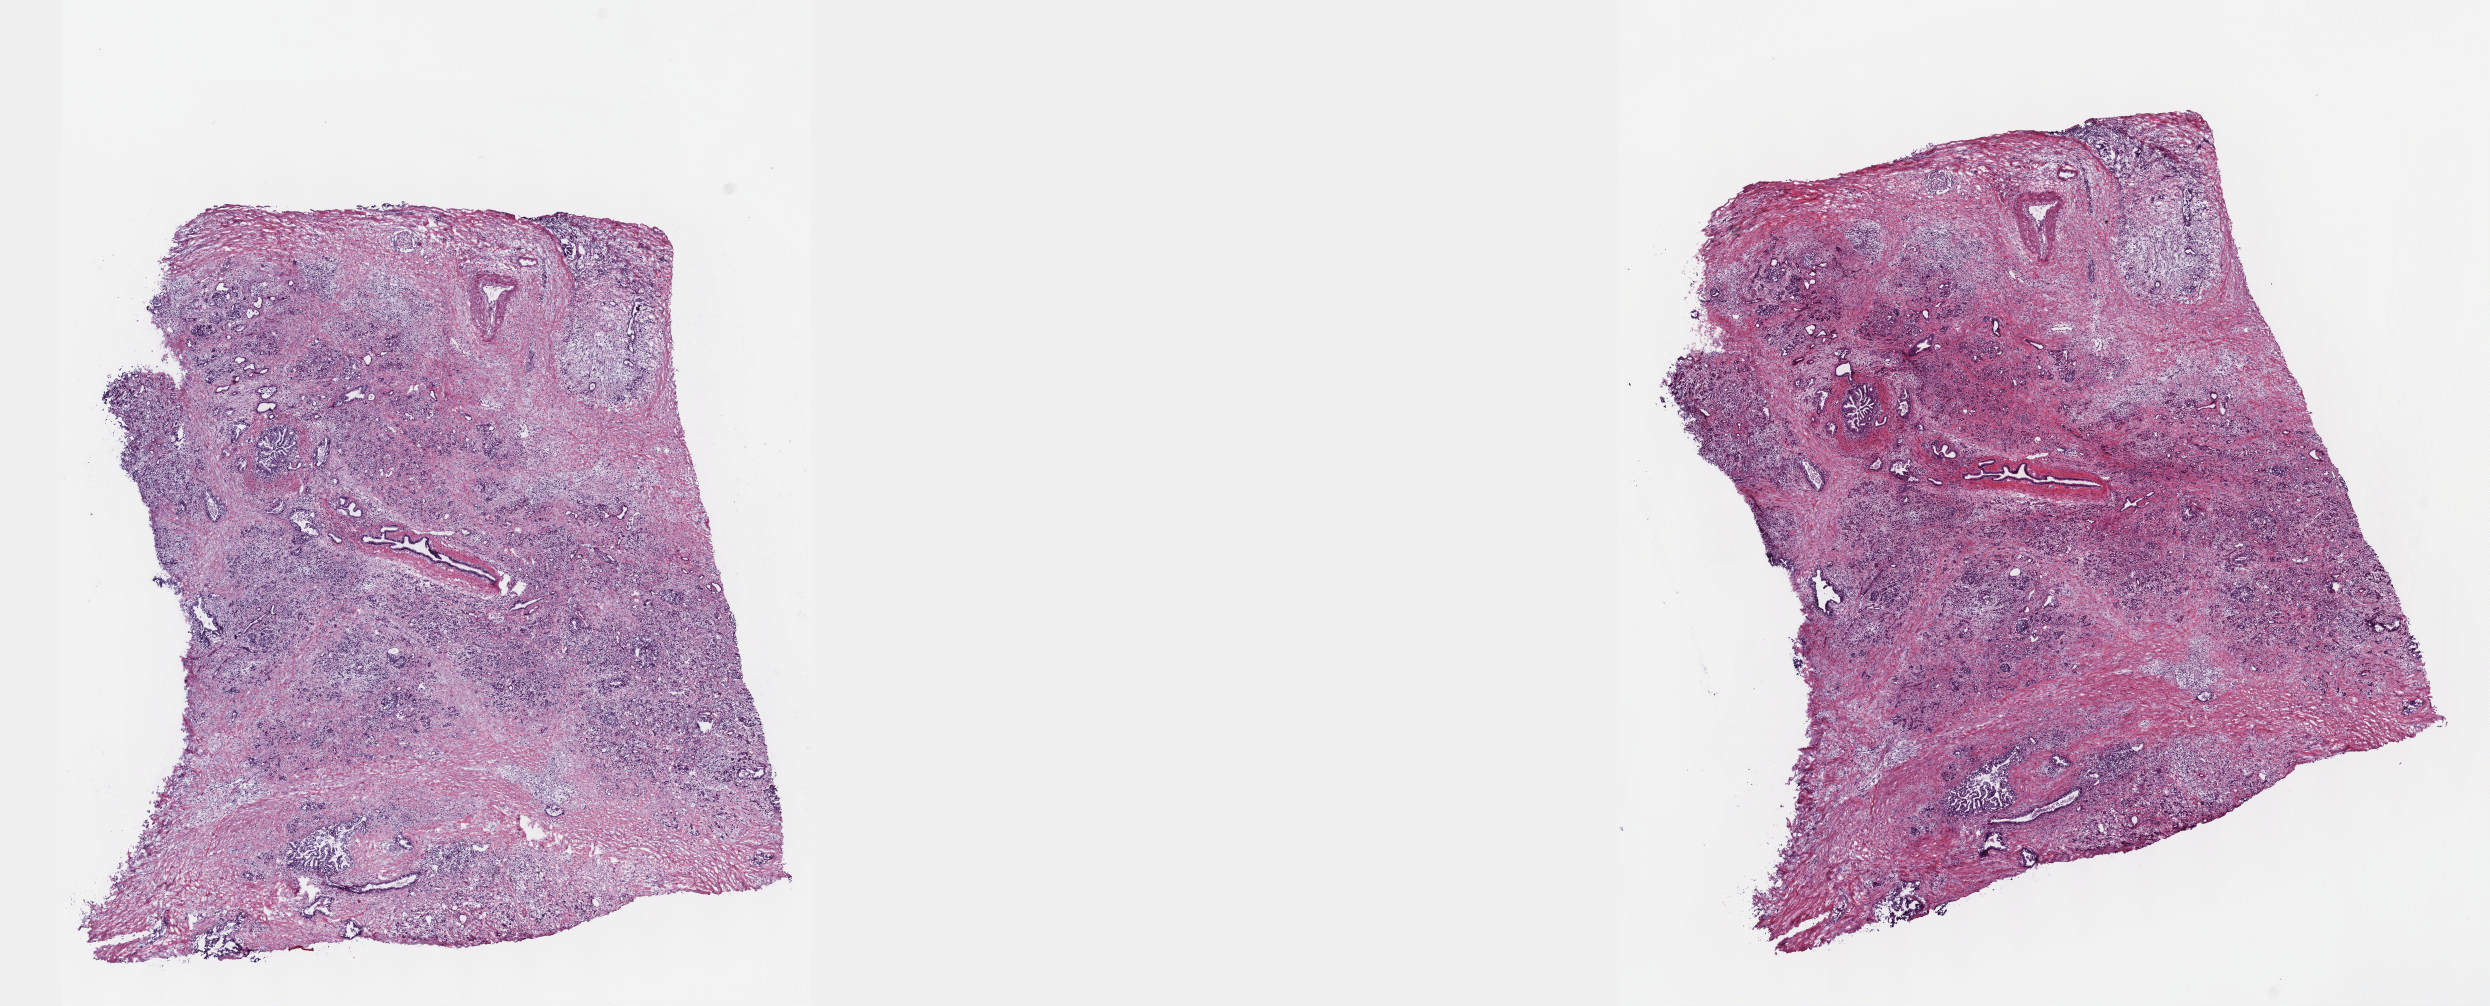
Digitized Hematoxylin and eosin (H&E) stained tissue section (whole slide), shown as a low-resolution overview of the whole scanned area (about 20.1 x 8.1 mm). Frozen section from the top of the tissue portion. Sample: primary tumour, pancreas. Male, age 48 years at initial diagnosis. Histologic grade: G2 (moderately differentiated). Slide review estimates, as recorded: tumour cells 40%, tumour nuclei 40%, normal cells 30%, stromal cells 30%, necrosis 0%. Infiltration values recorded for this section: lymphocyte infiltration 40%, monocyte infiltration 20%, neutrophil infiltration 20%.
* diagnosis: Adenocarcinoma, NOS (overlapping lesion of pancreas)
* AJCC pathologic stage: IIB (7th edition)
* lymph nodes positive (case pathology): 0 of 34 examined